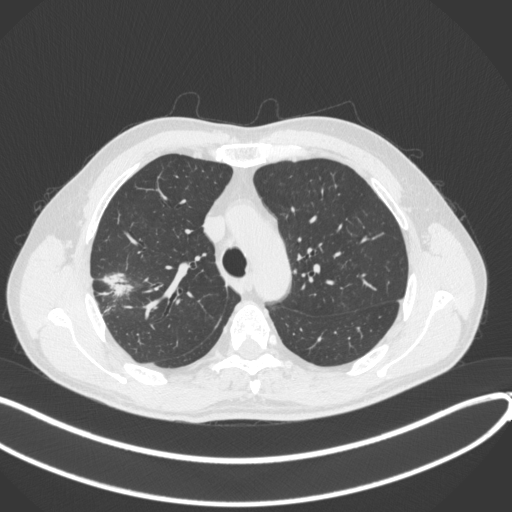
Chest CT, one axial slice. Slice 307 of 381 in the series (ordered by position). 120 kVp. Lung window (W 1500 / L -600 HU). 1 mm slice thickness. 512 × 512 image matrix, field of view 400 × 400 mm. Male patient, age 62 years. From the clinical record (not read from this slice): clinical TNM (as recorded): T1c N0 M0; histopathological grade: G2-3.
Annotated regions visible in this slice (bounding box drawn by a radiologist):
- lung tumour (recorded histology: adenocarcinoma): bounding box (x1, y1, x2, y2) in pixels: (101, 268, 130, 301)